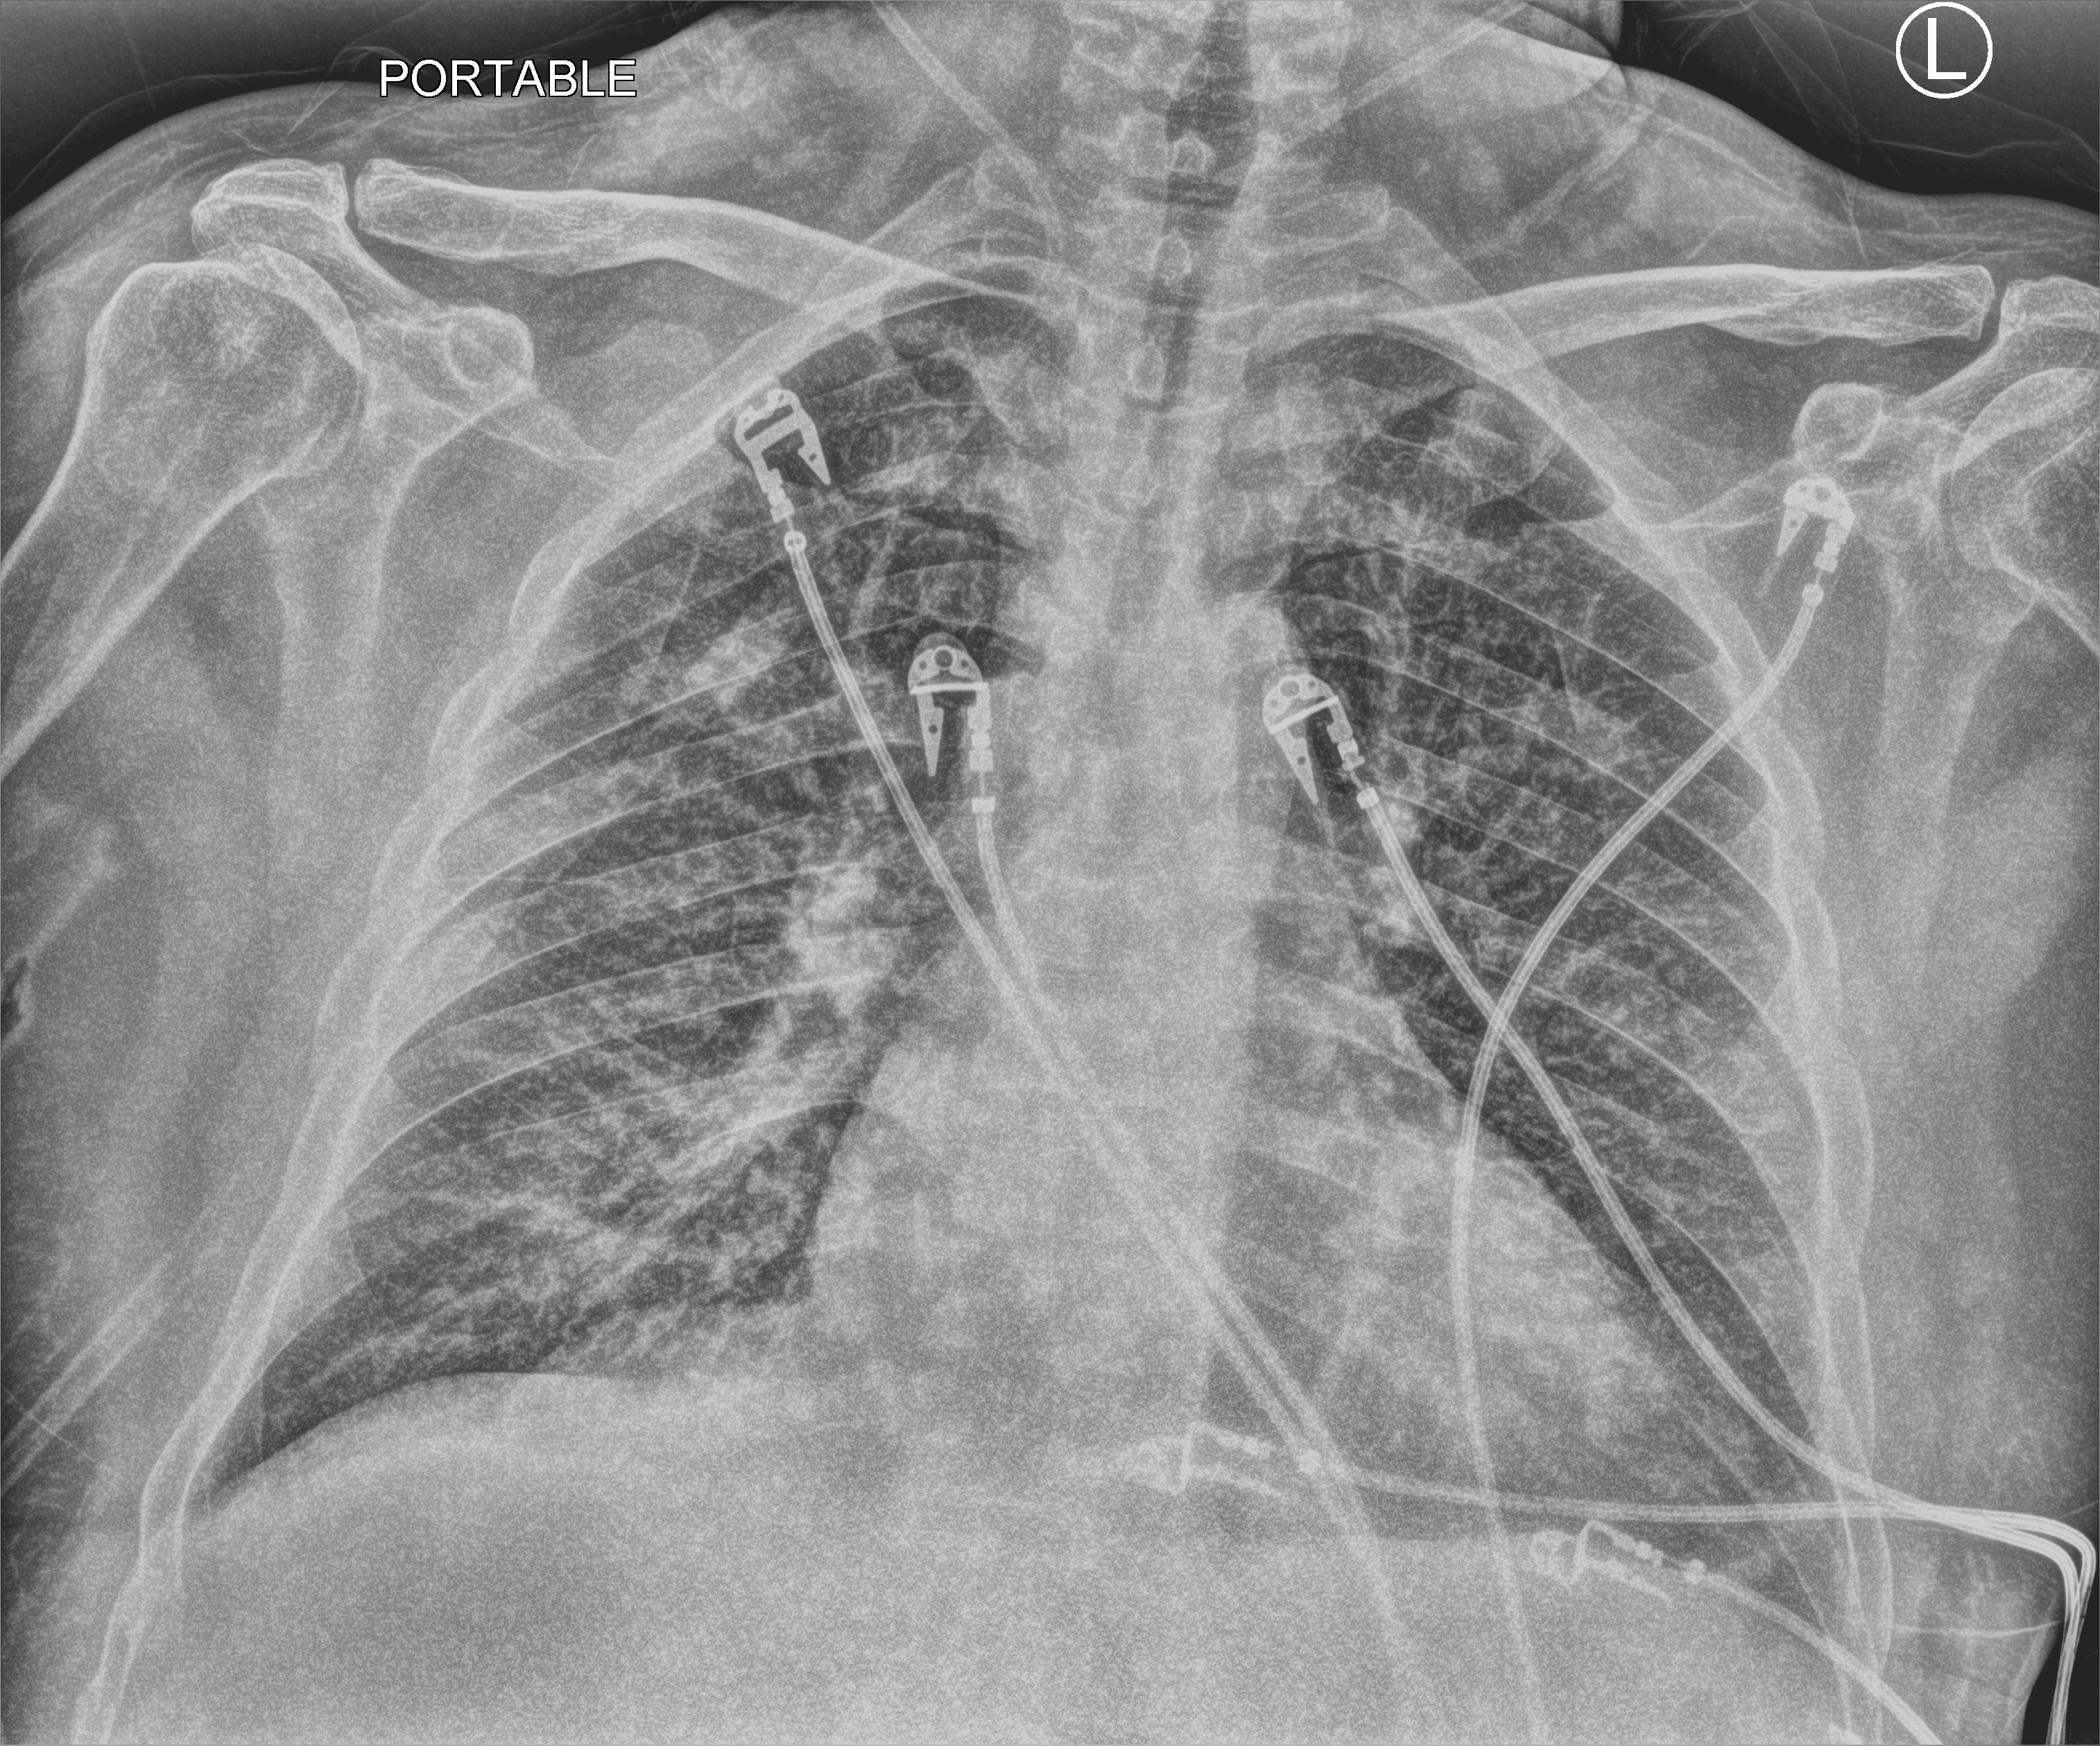
Portable chest radiograph, anteroposterior (AP) projection. Male patient hospitalised with COVID-19, age 60–74 years.
Hospital-stay facts (about this admission, not read from this image; timing relative to this image not recorded):
- admitted to intensive care during this hospital stay: no
- mechanically ventilated during this hospital stay: no